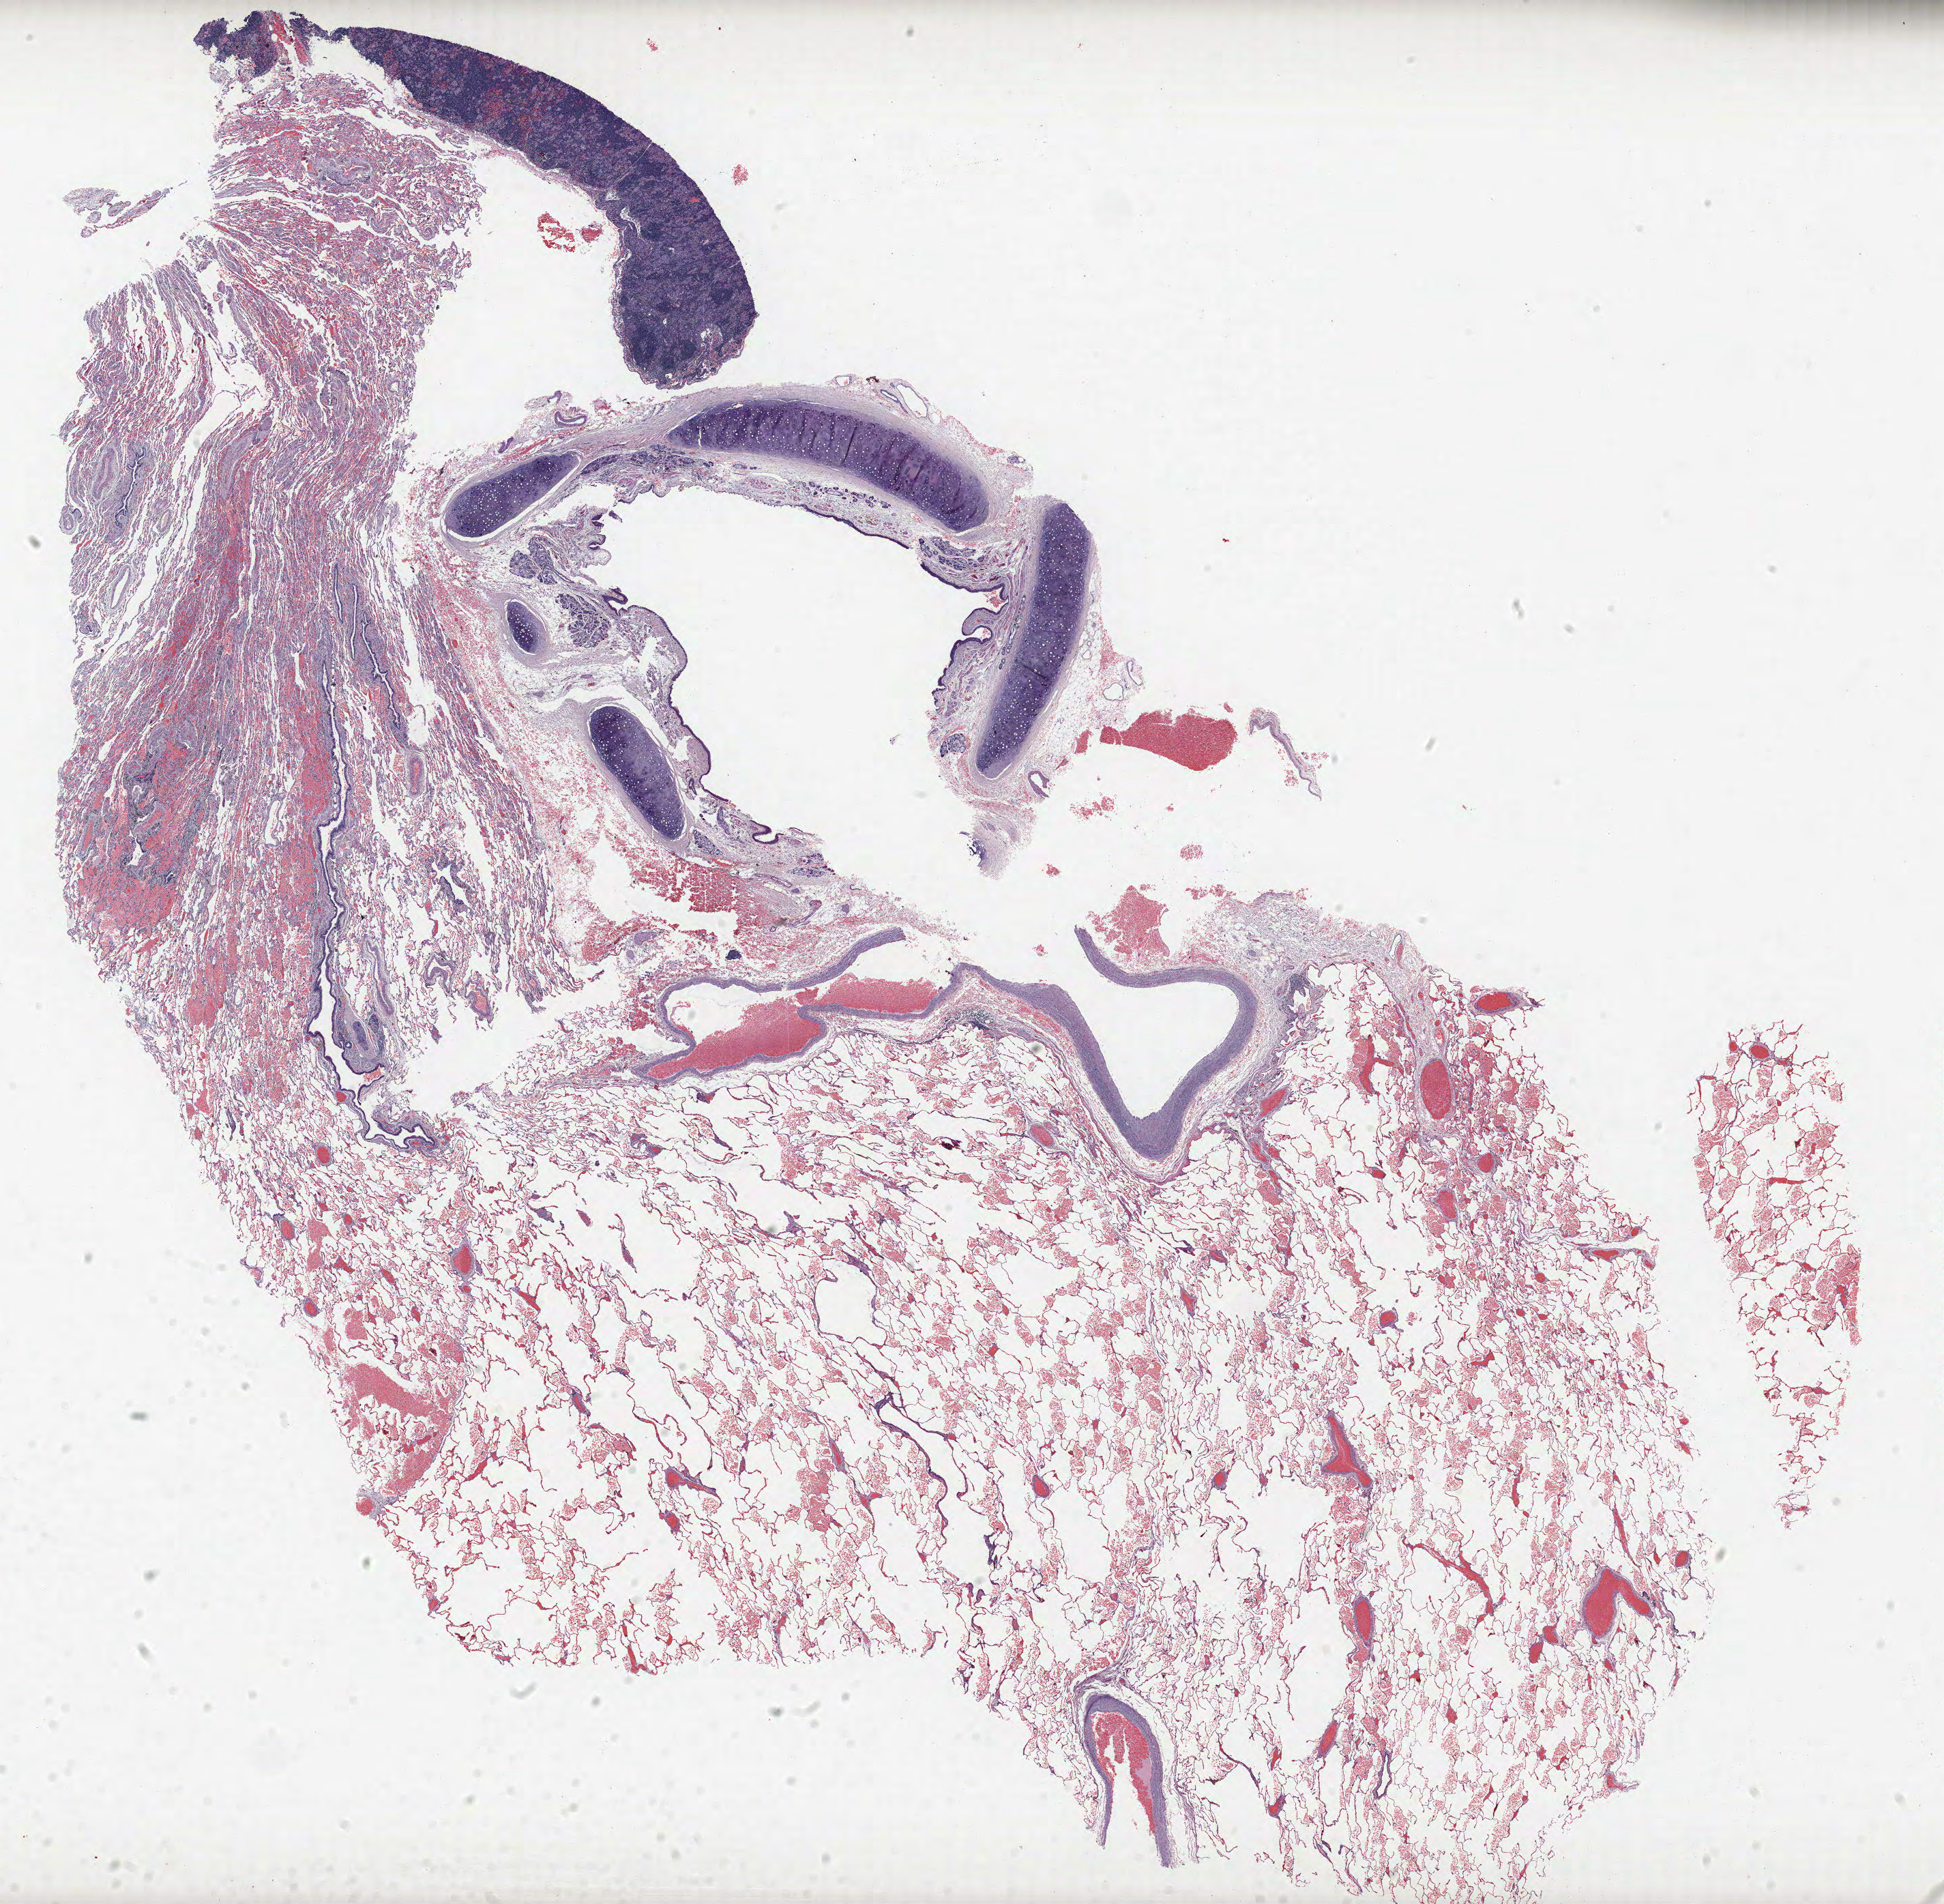
Whole-slide histology image, H&E-stained, shown as a low-resolution overview of the whole scanned area (about 22.8 x 22.3 mm, from a 40x scan). FFPE section. Lung. Male, age 61 at enrolment. Former smoker at enrolment. Grade: poorly differentiated (G3).
- participant's lung-cancer diagnosis: Squamous cell carcinoma, NOS
- stage (AJCC 6th edition): IA
- tumour size (pathology): 20 mm
- primary tumour location (clinical record): right upper lobe